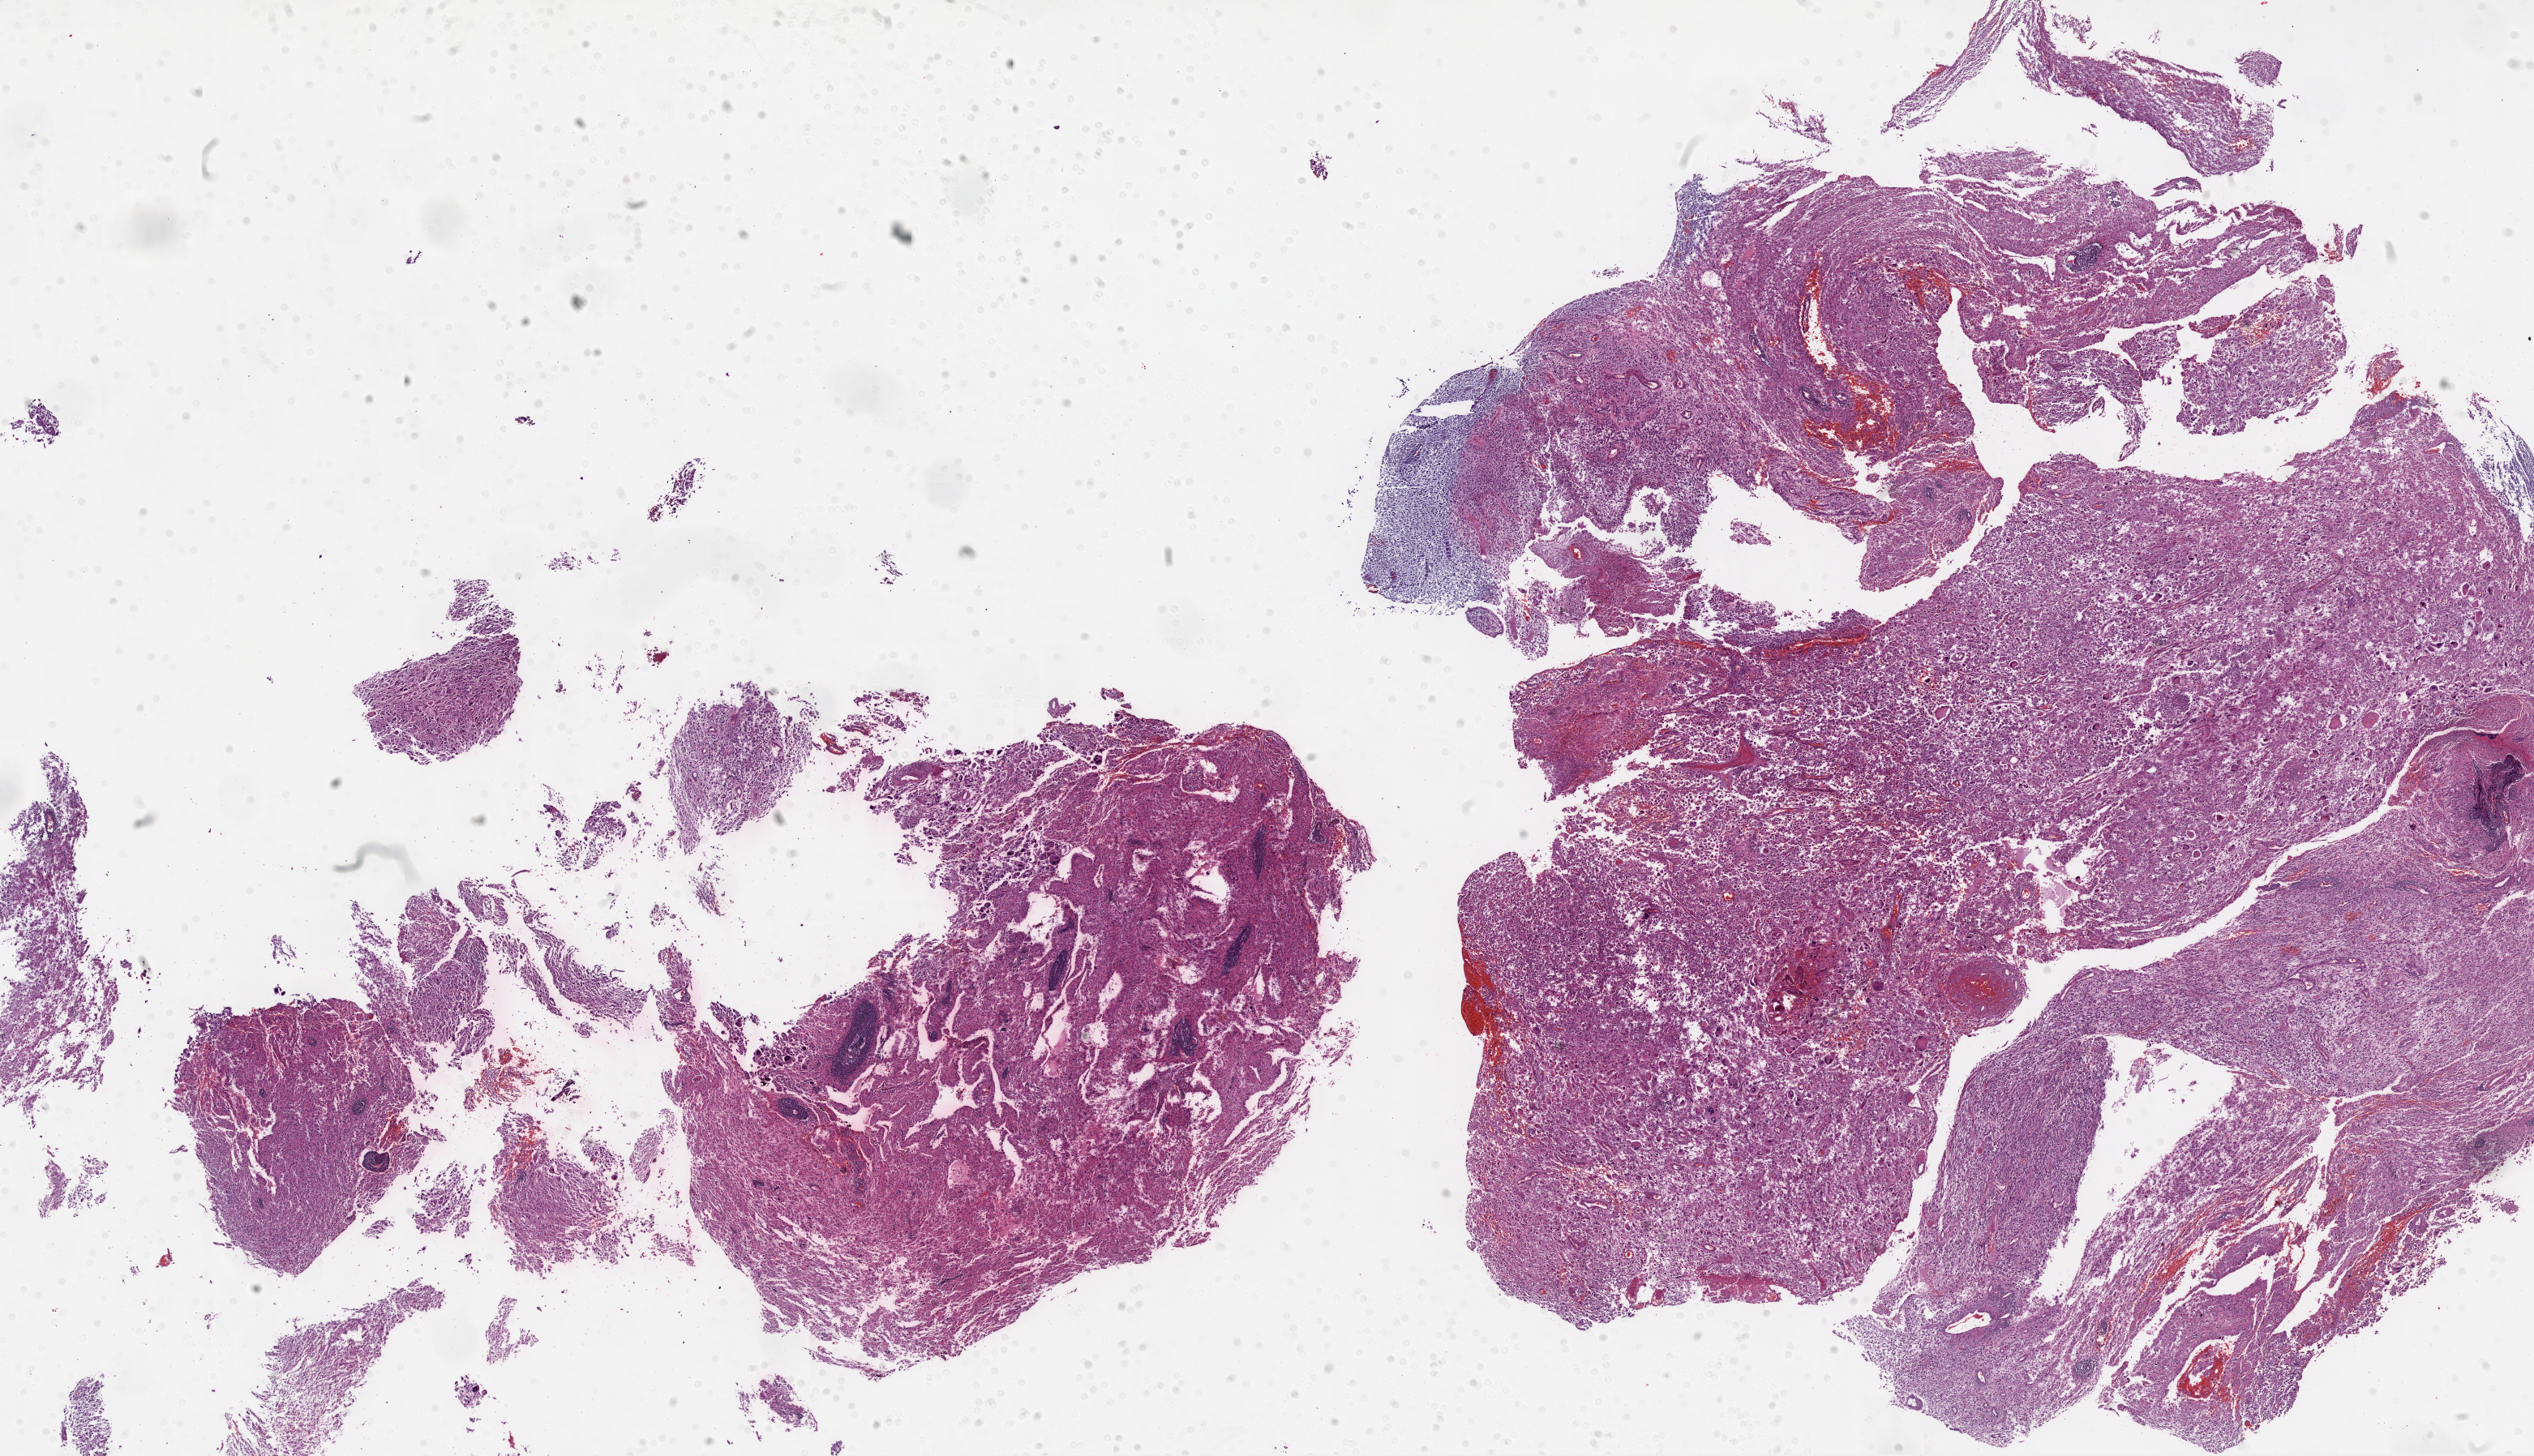
Digitized Hematoxylin and eosin (H&E) stained tissue section (whole slide) — whole scanned area (about 25.1 x 14.4 mm, acquisition: 20x scan) shown as a low-resolution overview; formalin-fixed paraffin-embedded (FFPE) diagnostic section; brain, primary tumour sample. Patient: female, age at initial diagnosis 51 years.
• pathologic diagnosis: Glioblastoma